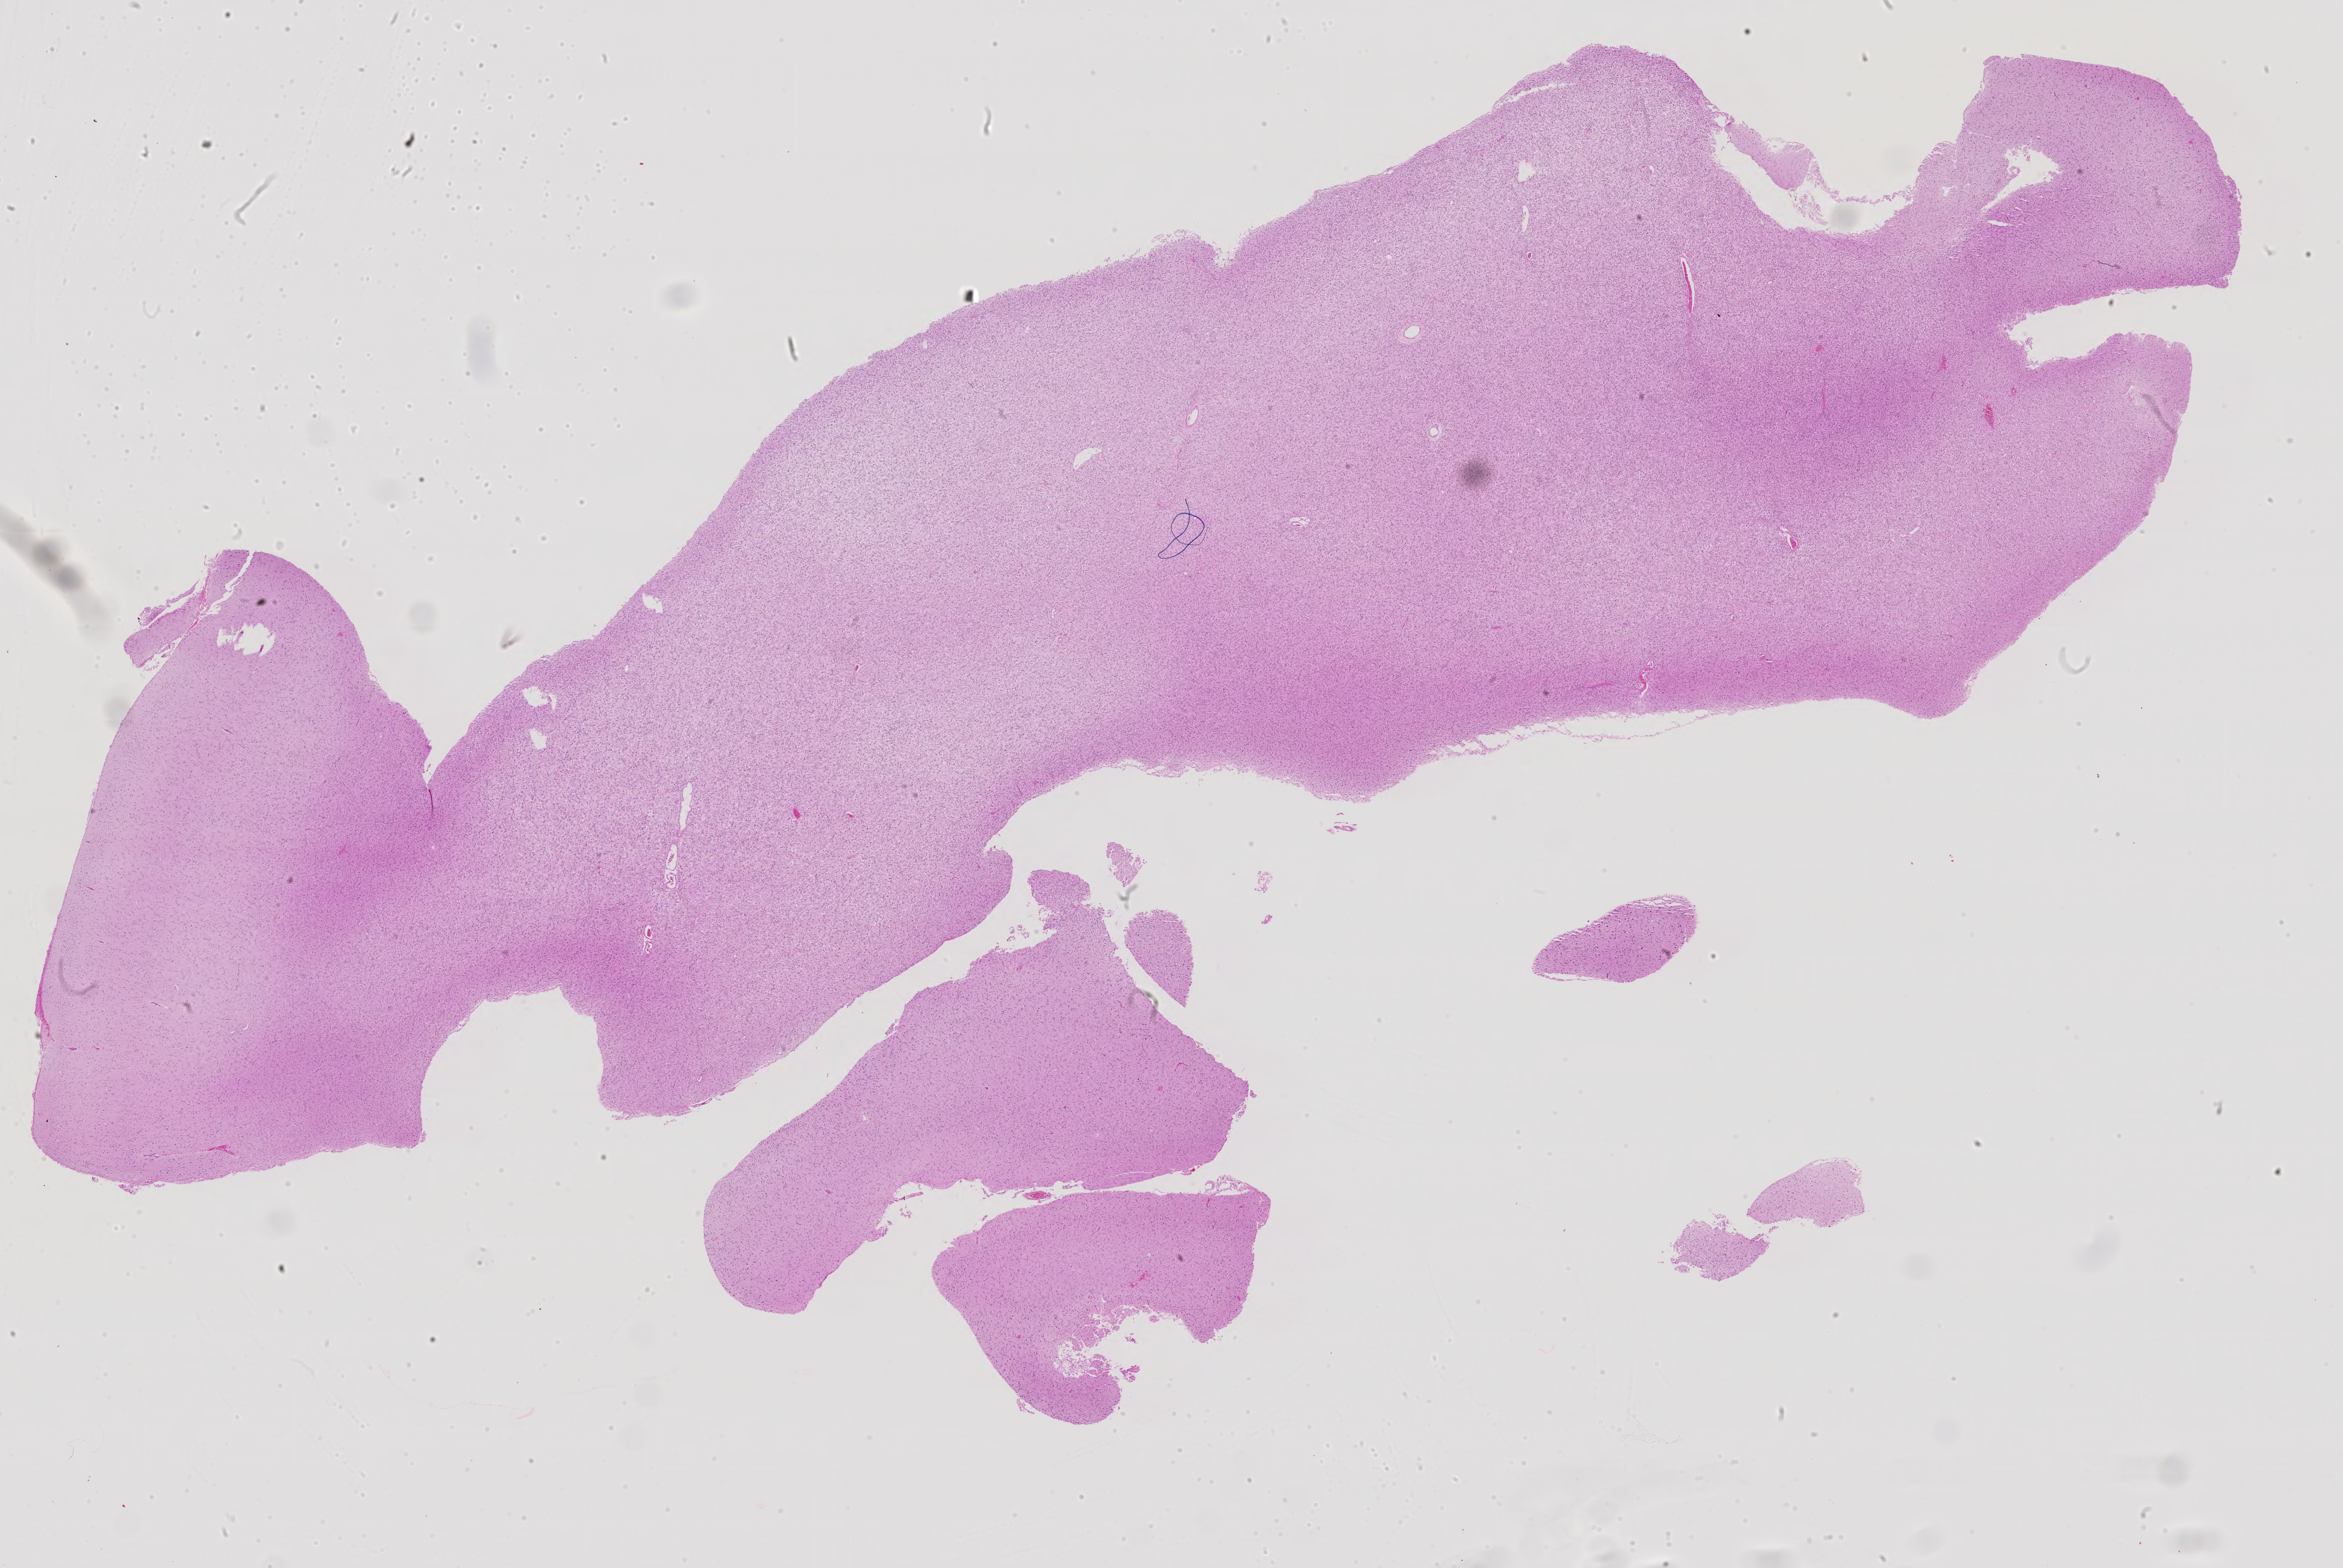
Digitized H&E tissue section (whole slide), shown as a low-resolution overview of the whole scanned area (about 31.3 x 21.0 mm, acquisition: 40x scan). Formalin-fixed paraffin-embedded (FFPE) diagnostic section. Primary tumour sample from the brain. Female patient; age at initial diagnosis 47 years. Histologic grade: G3 (poorly differentiated).
- histologic diagnosis: Astrocytoma, anaplastic (cerebrum)
- laterality: right